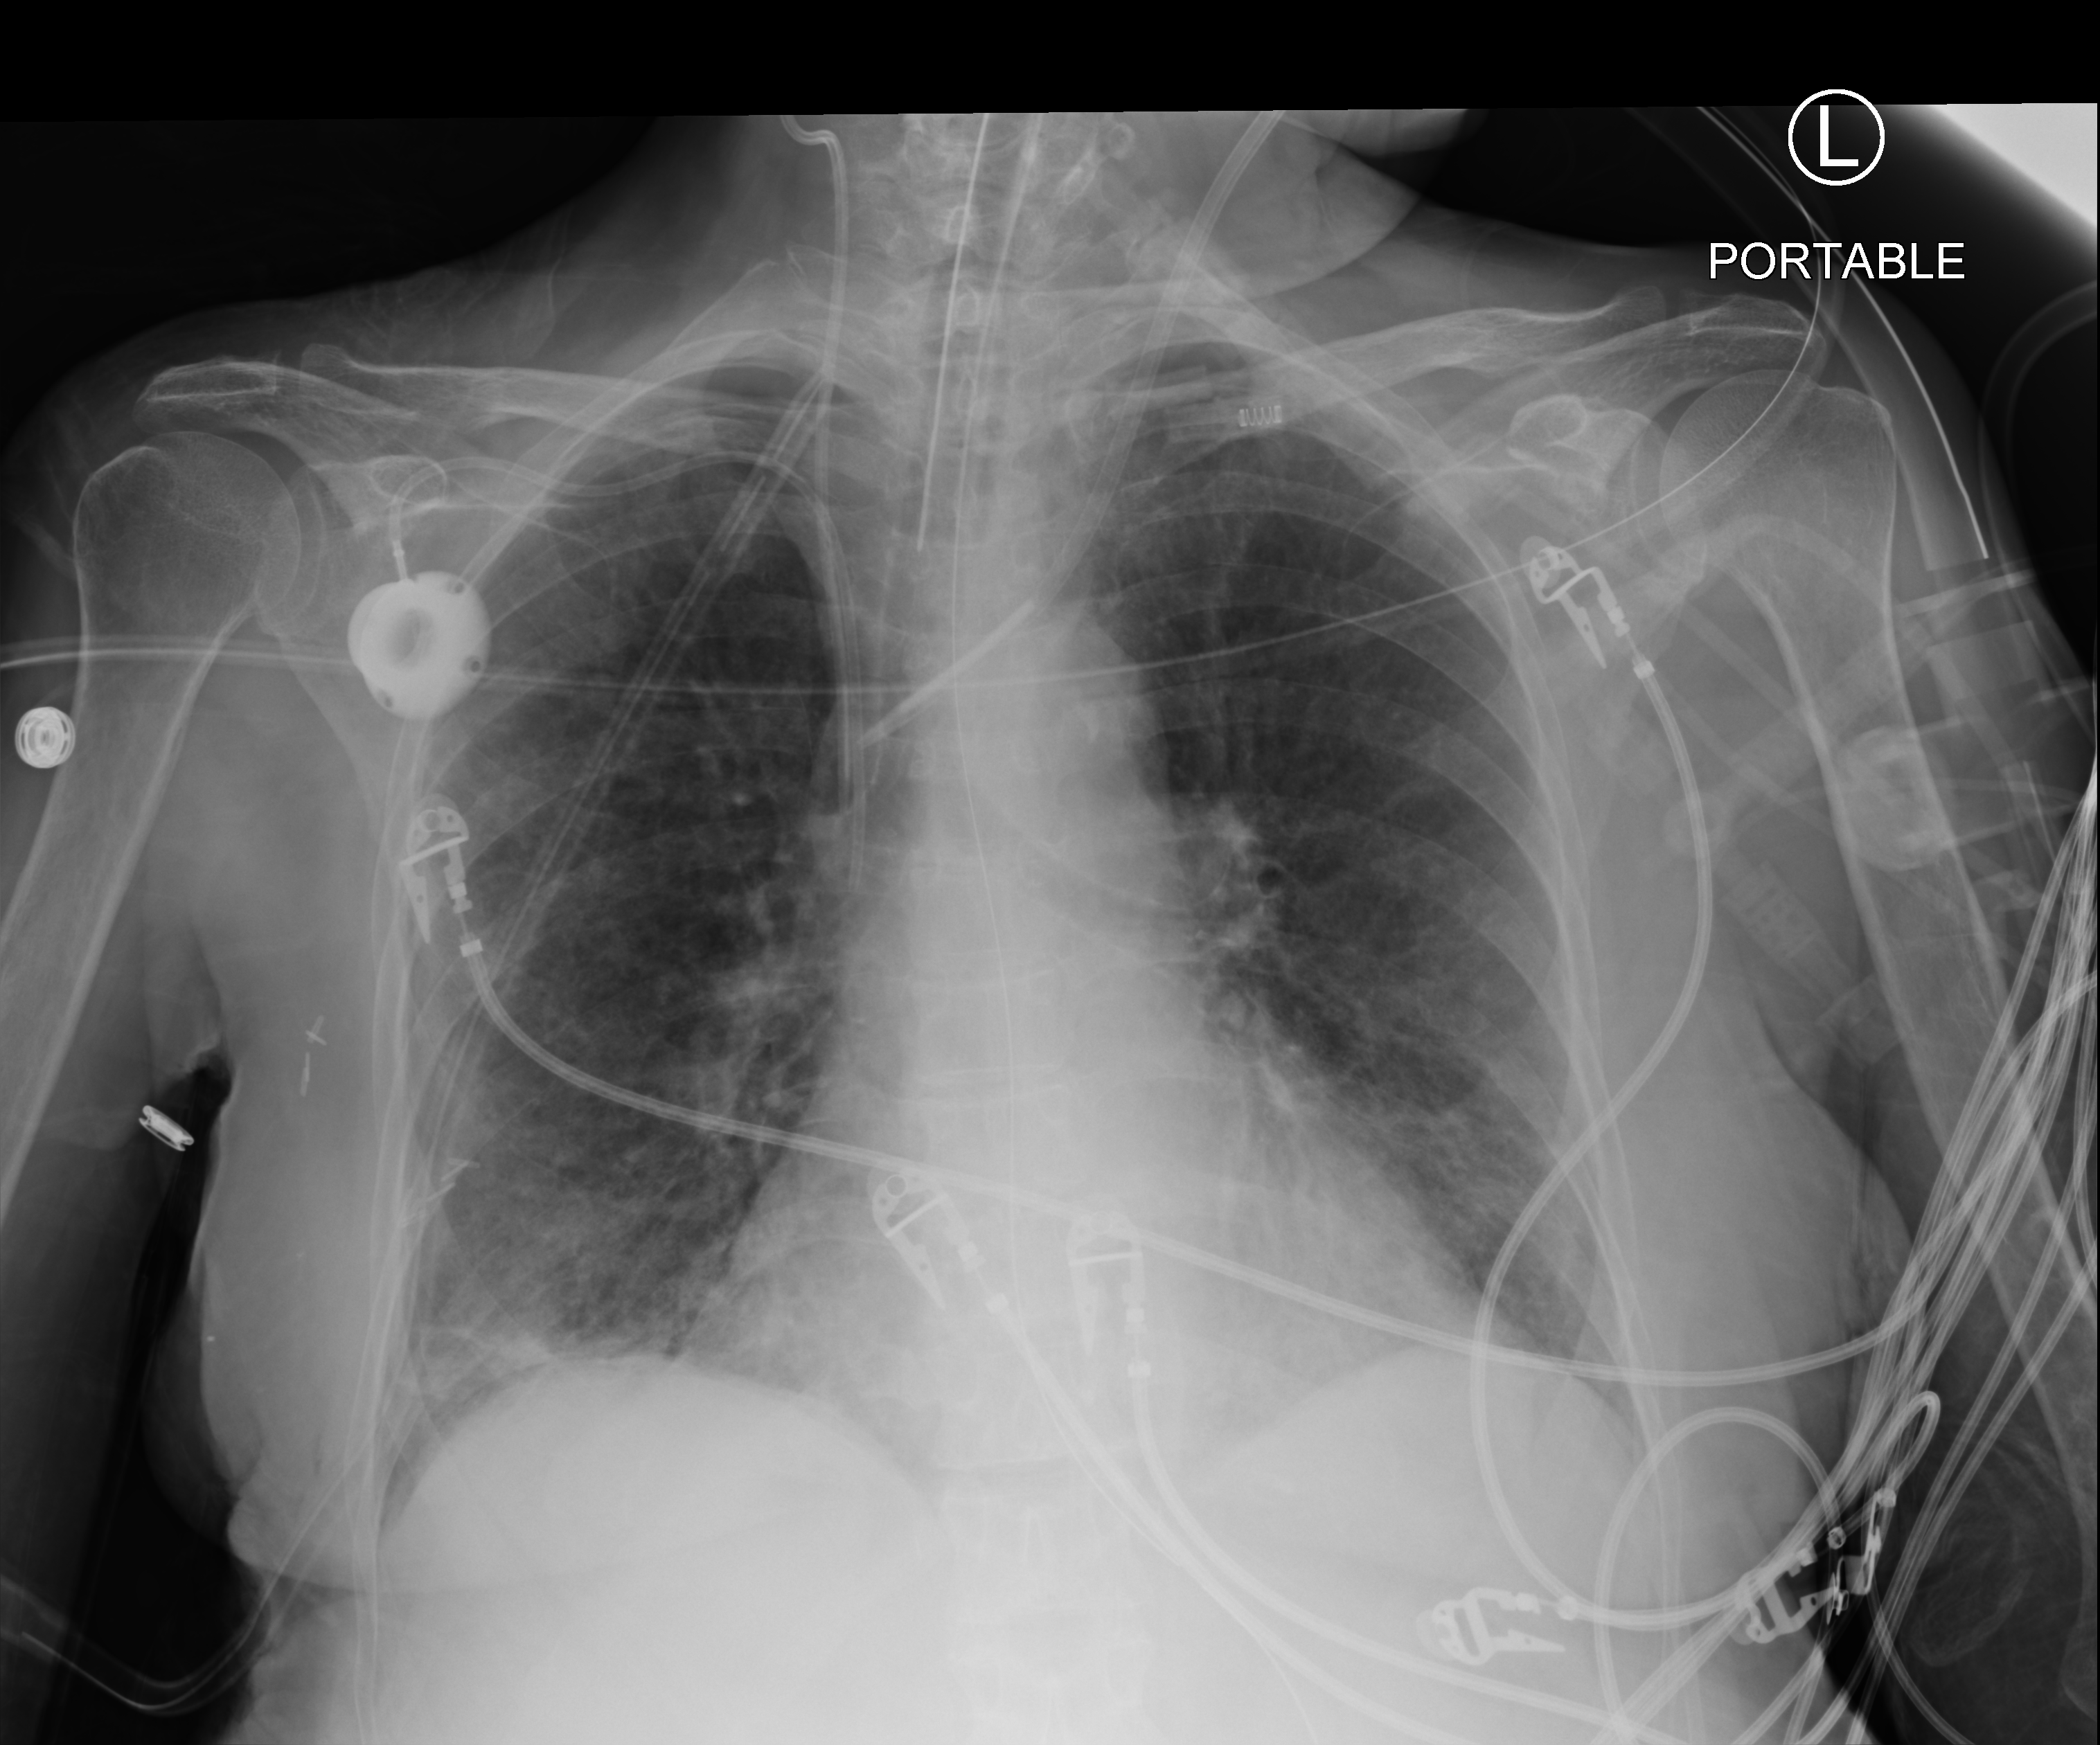
Bedside chest radiograph (computed radiography), anteroposterior (AP) projection. Patient hospitalised with COVID-19; female, aged 60–74 years.
From the hospital-stay record, not from the radiograph (when in the stay this image was taken is not recorded): mechanically ventilated during this hospital stay: yes; COPD (admission record): no; admitted to intensive care during this hospital stay: yes.